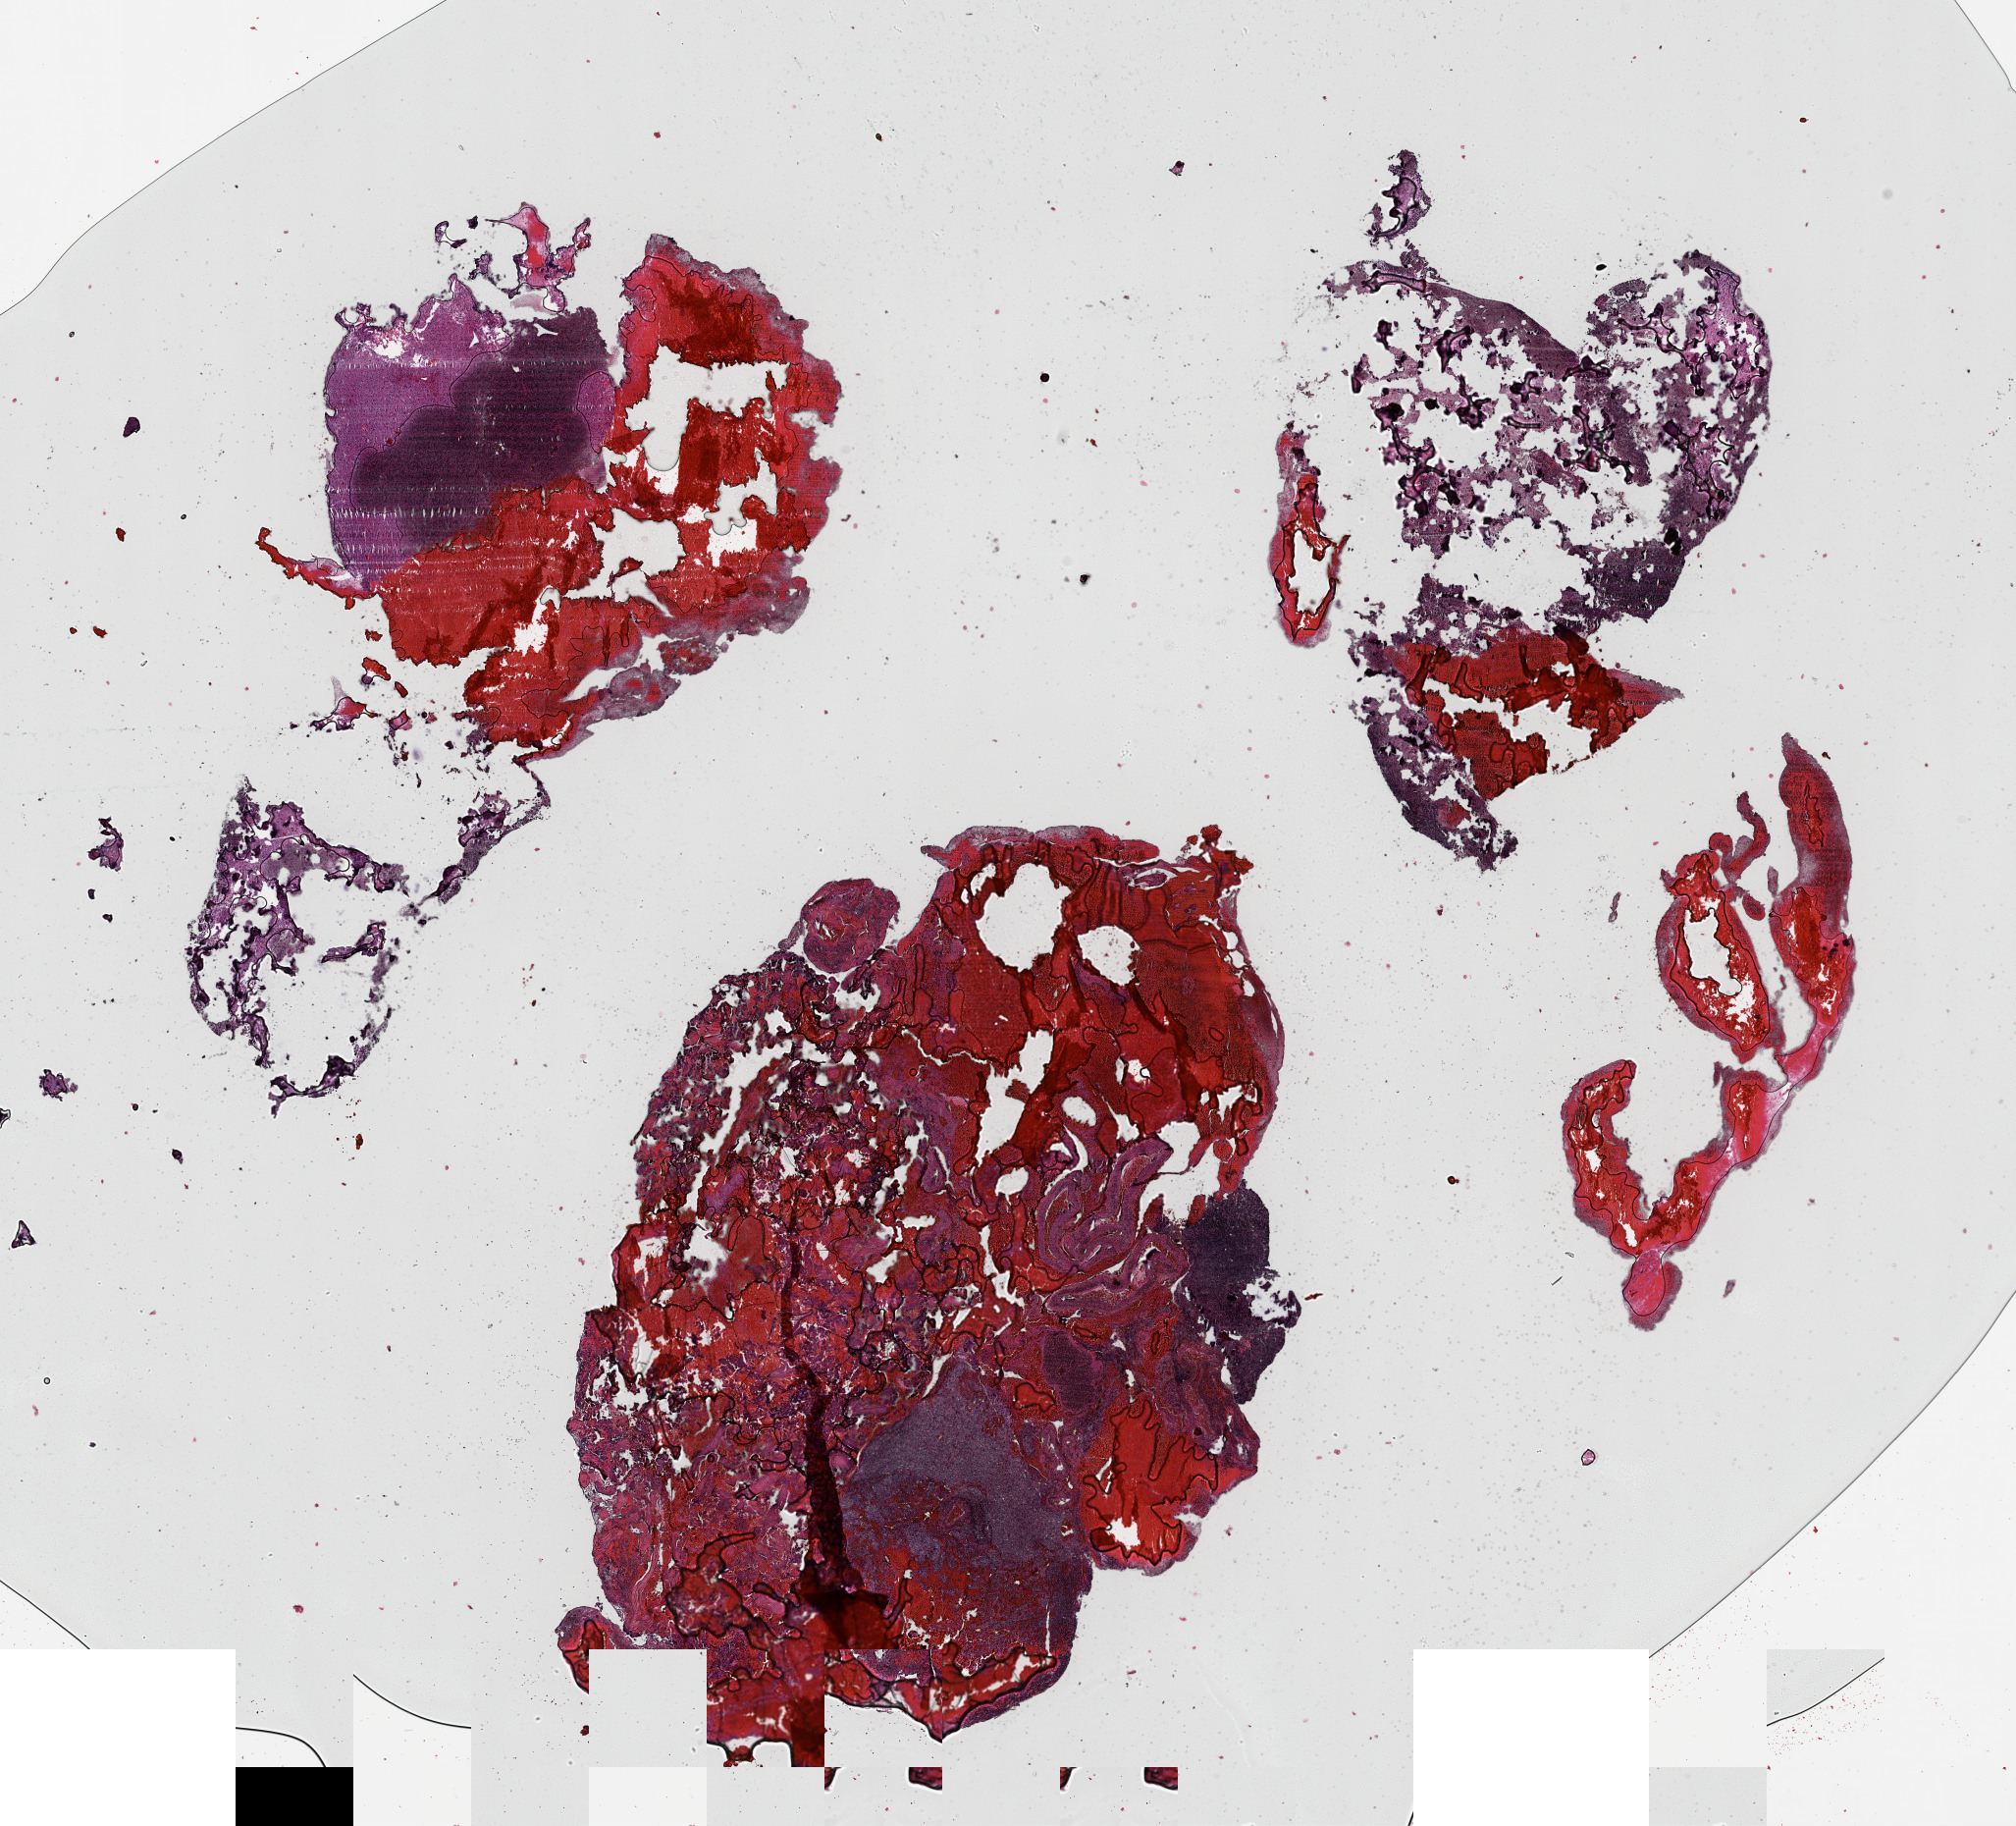
Hematoxylin and eosin (H&E) stained whole-slide image — shown as a low-resolution overview of the whole scanned area (about 16.6 x 15.0 mm, acquisition: 40x scan); FFPE section; brain, primary tumour sample. Male patient; age at initial diagnosis 74 years.
Histologic diagnosis: Oligodendroglioma, anaplastic (cerebrum).